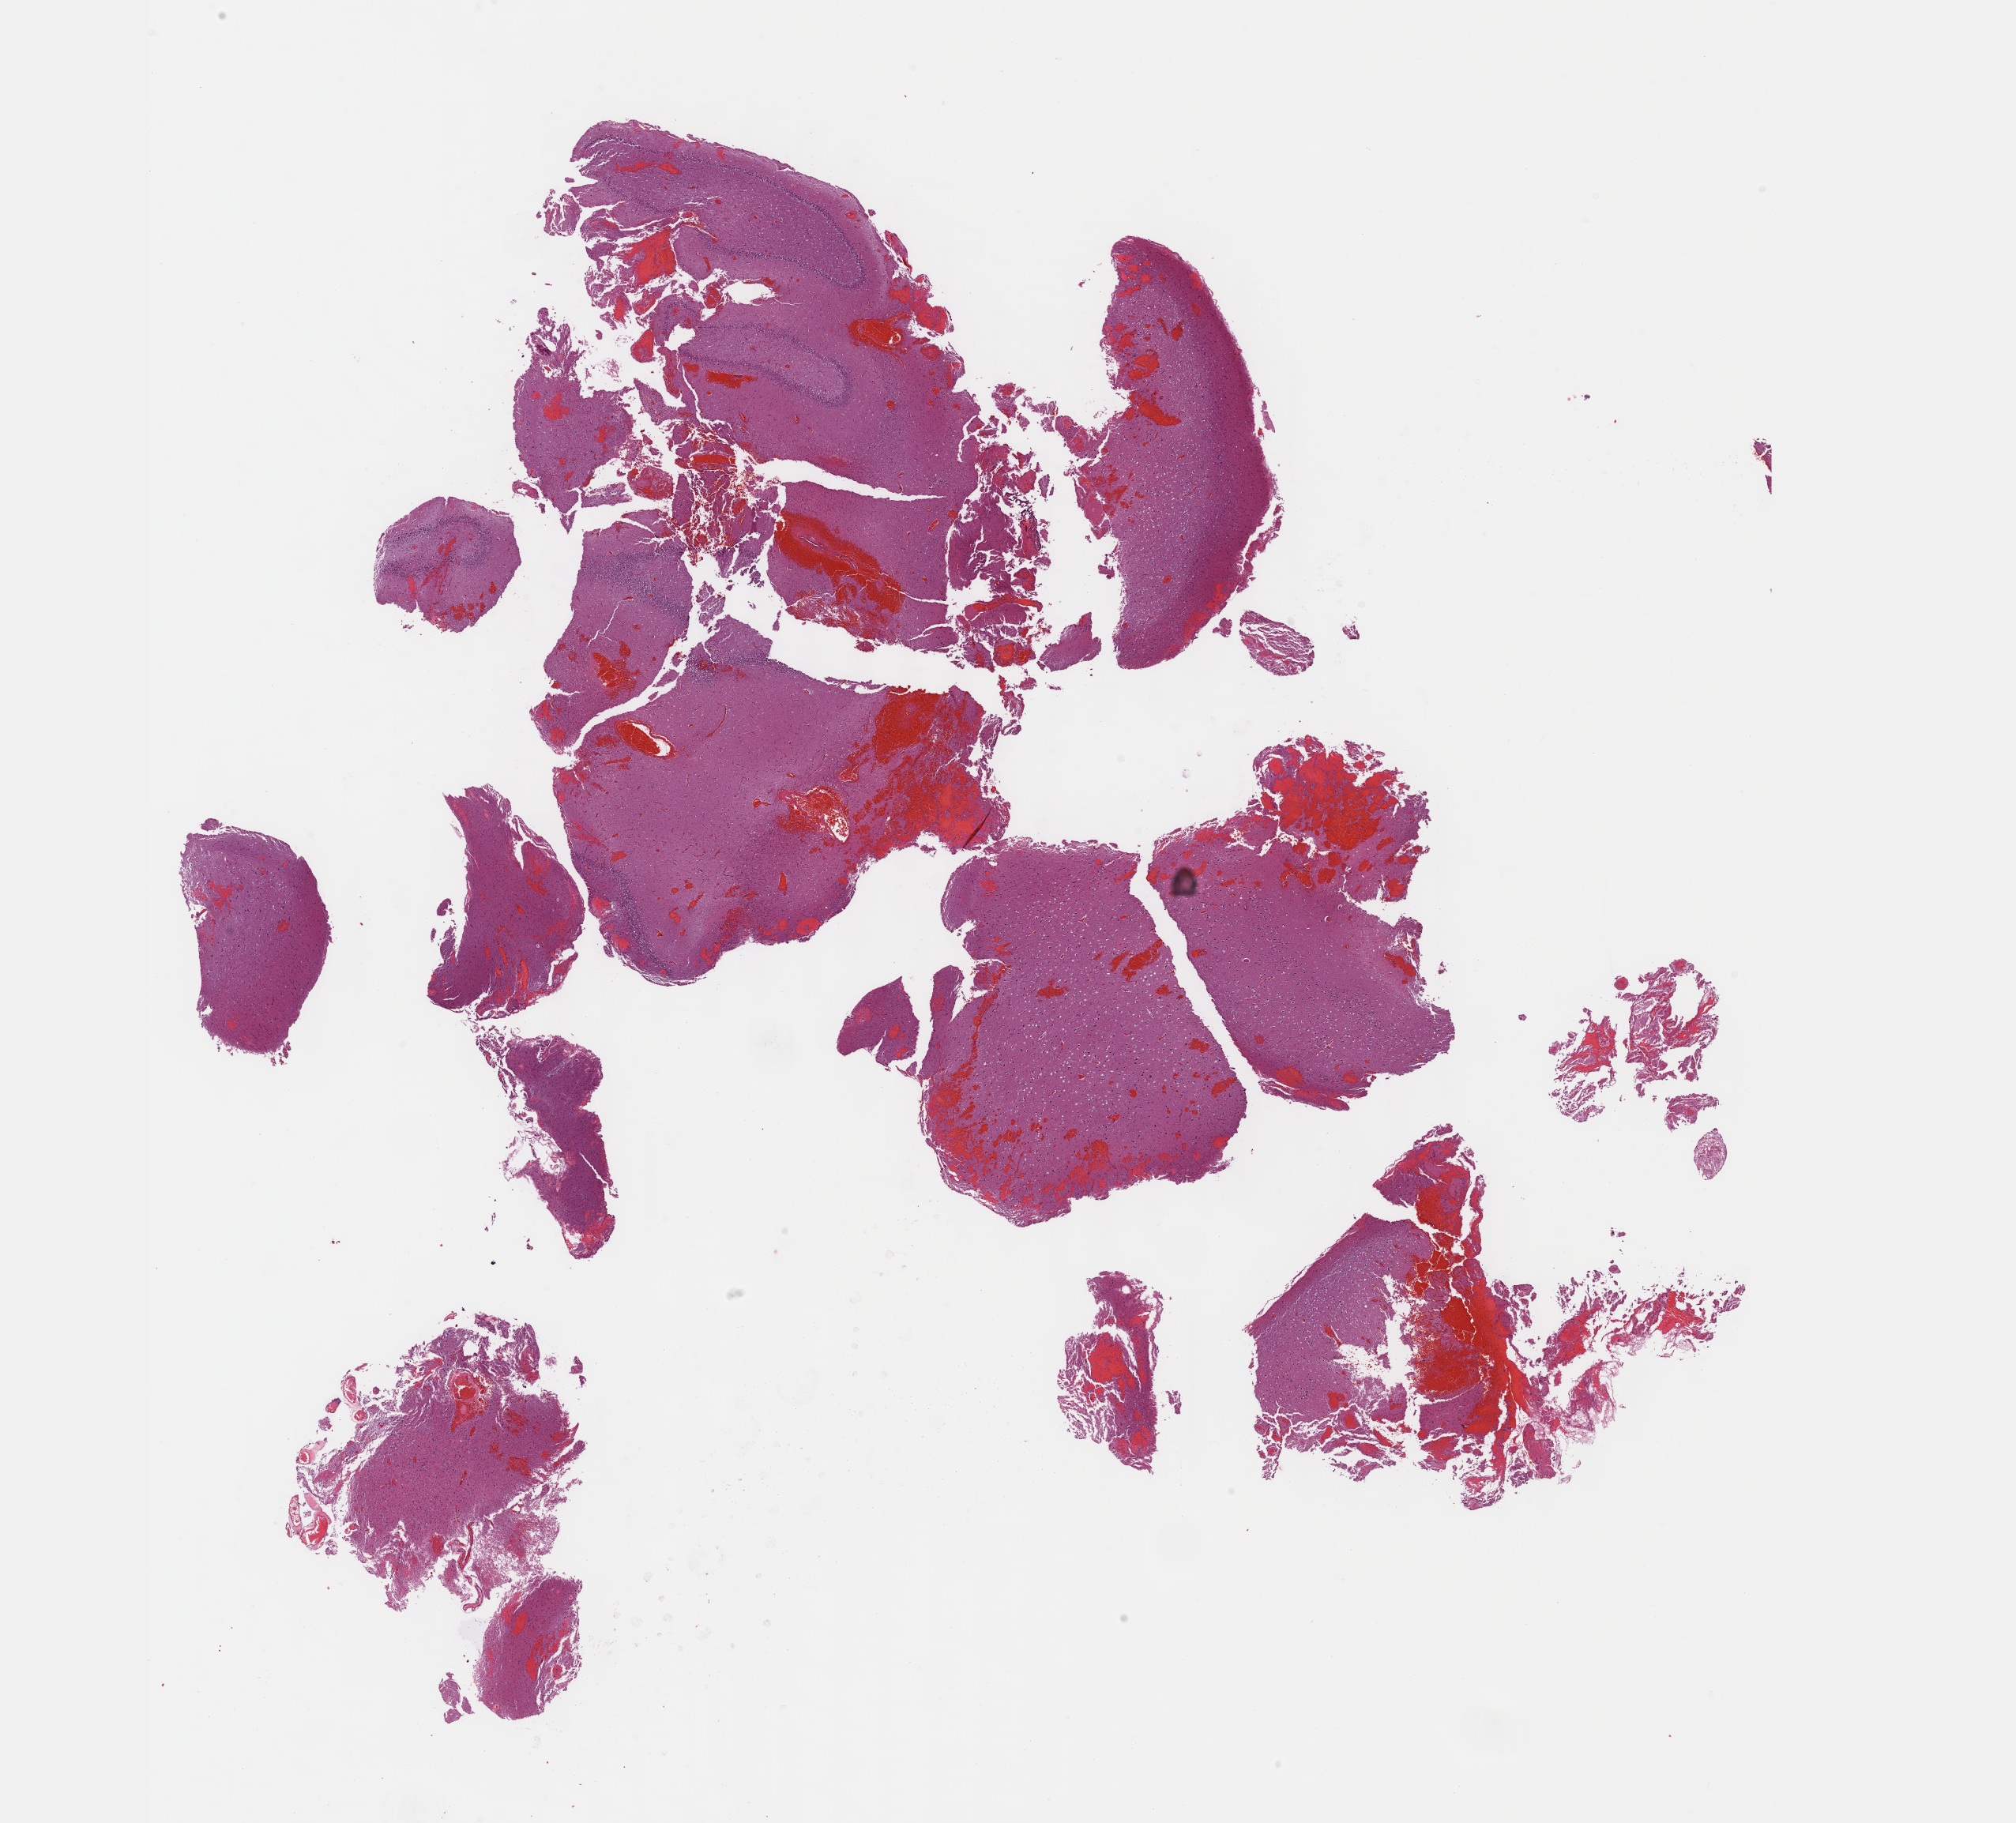
H&E whole-slide image, whole scanned area (about 20.6 x 18.7 mm) shown as a low-resolution overview, formalin-fixed paraffin-embedded (FFPE) diagnostic section, primary tumour sample from the brain. Male, age 38 years at initial diagnosis. Histologic grade: G2 (moderately differentiated).
Pathologic diagnosis: Oligodendroglioma, NOS (cerebrum). Laterality: left.